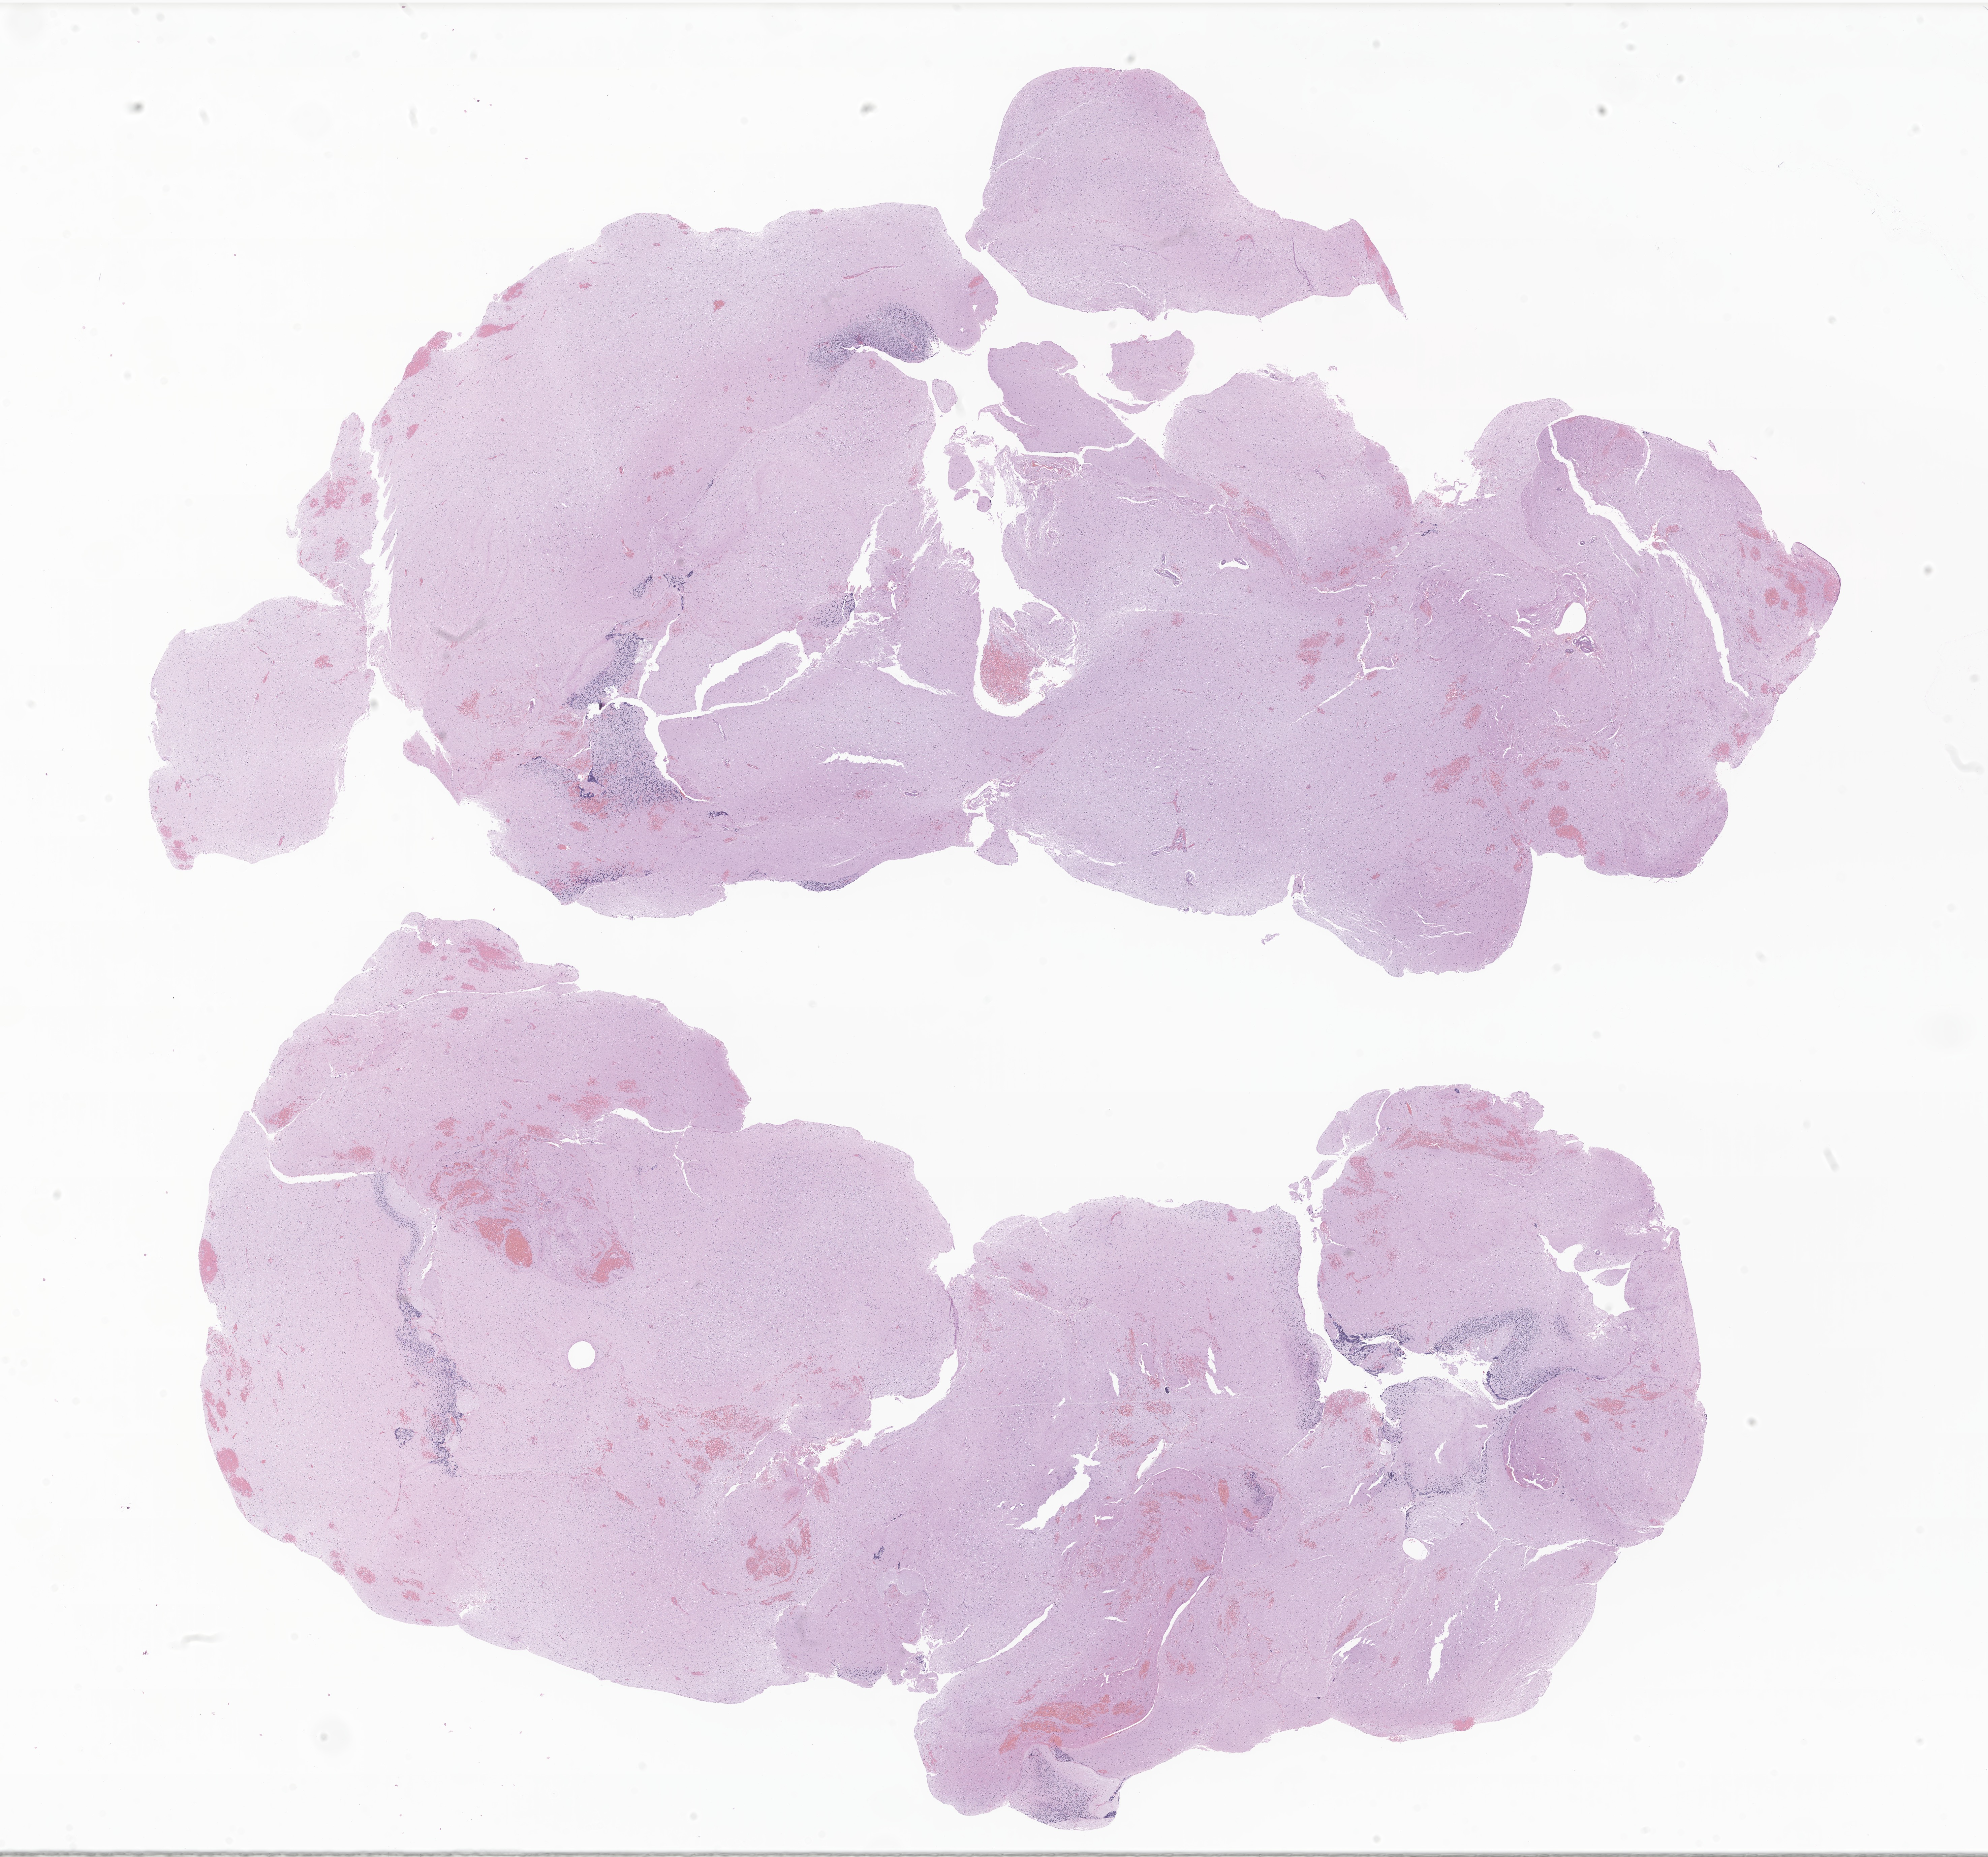
Digitized hematoxylin and eosin (H&E)-stained section of tumor tissue from the brain, whole scanned area (about 24.9 x 23.2 mm) shown as a low-resolution overview, FFPE section. Patient male; age 61 months (5 years 1 month).
Diagnosis (ICD-O-3 morphology term): Glioma, malignant.